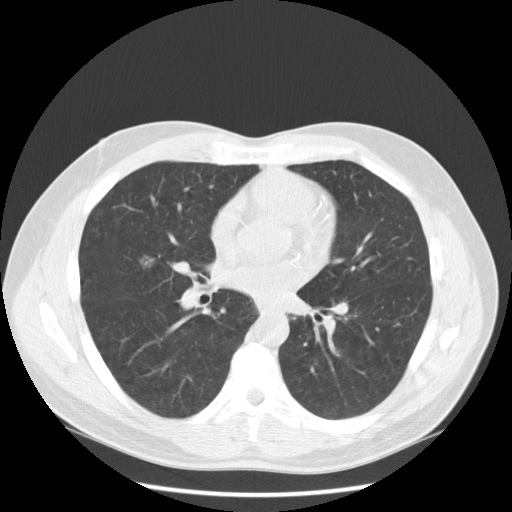
Low-dose screening chest CT, one axial slice. Position 110 of 234 along the scan axis. Reconstruction kernel STANDARD. 120 kVp. Lung window (W 1500 / L -600 HU). 2.5 mm slice thickness. 512 × 512 image matrix, field of view 385 × 385 mm.
Annotated regions visible in this slice (expert manual segmentation):
- lesion 1 (tumor, middle lobe of right lung): bounding box <139,254,156,268> (left, top, right, bottom; pixels)